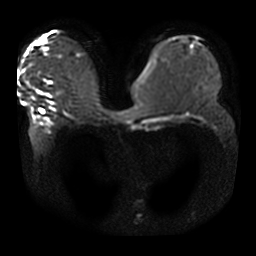
Breast MRI, one axial slice. Position 19 of 42 along the scan axis. Diffusion-weighted series; image 2 of 4 stored at this slice position (different b-values; order by instance number). 3 T. 5 mm slice thickness. 256 × 256 image matrix. Female patient.
Annotated regions visible in this slice (expert manual segmentation):
- tumour on diffusion-weighted imaging: bounding box (x1, y1, x2, y2) in pixels: (37, 90, 42, 94)